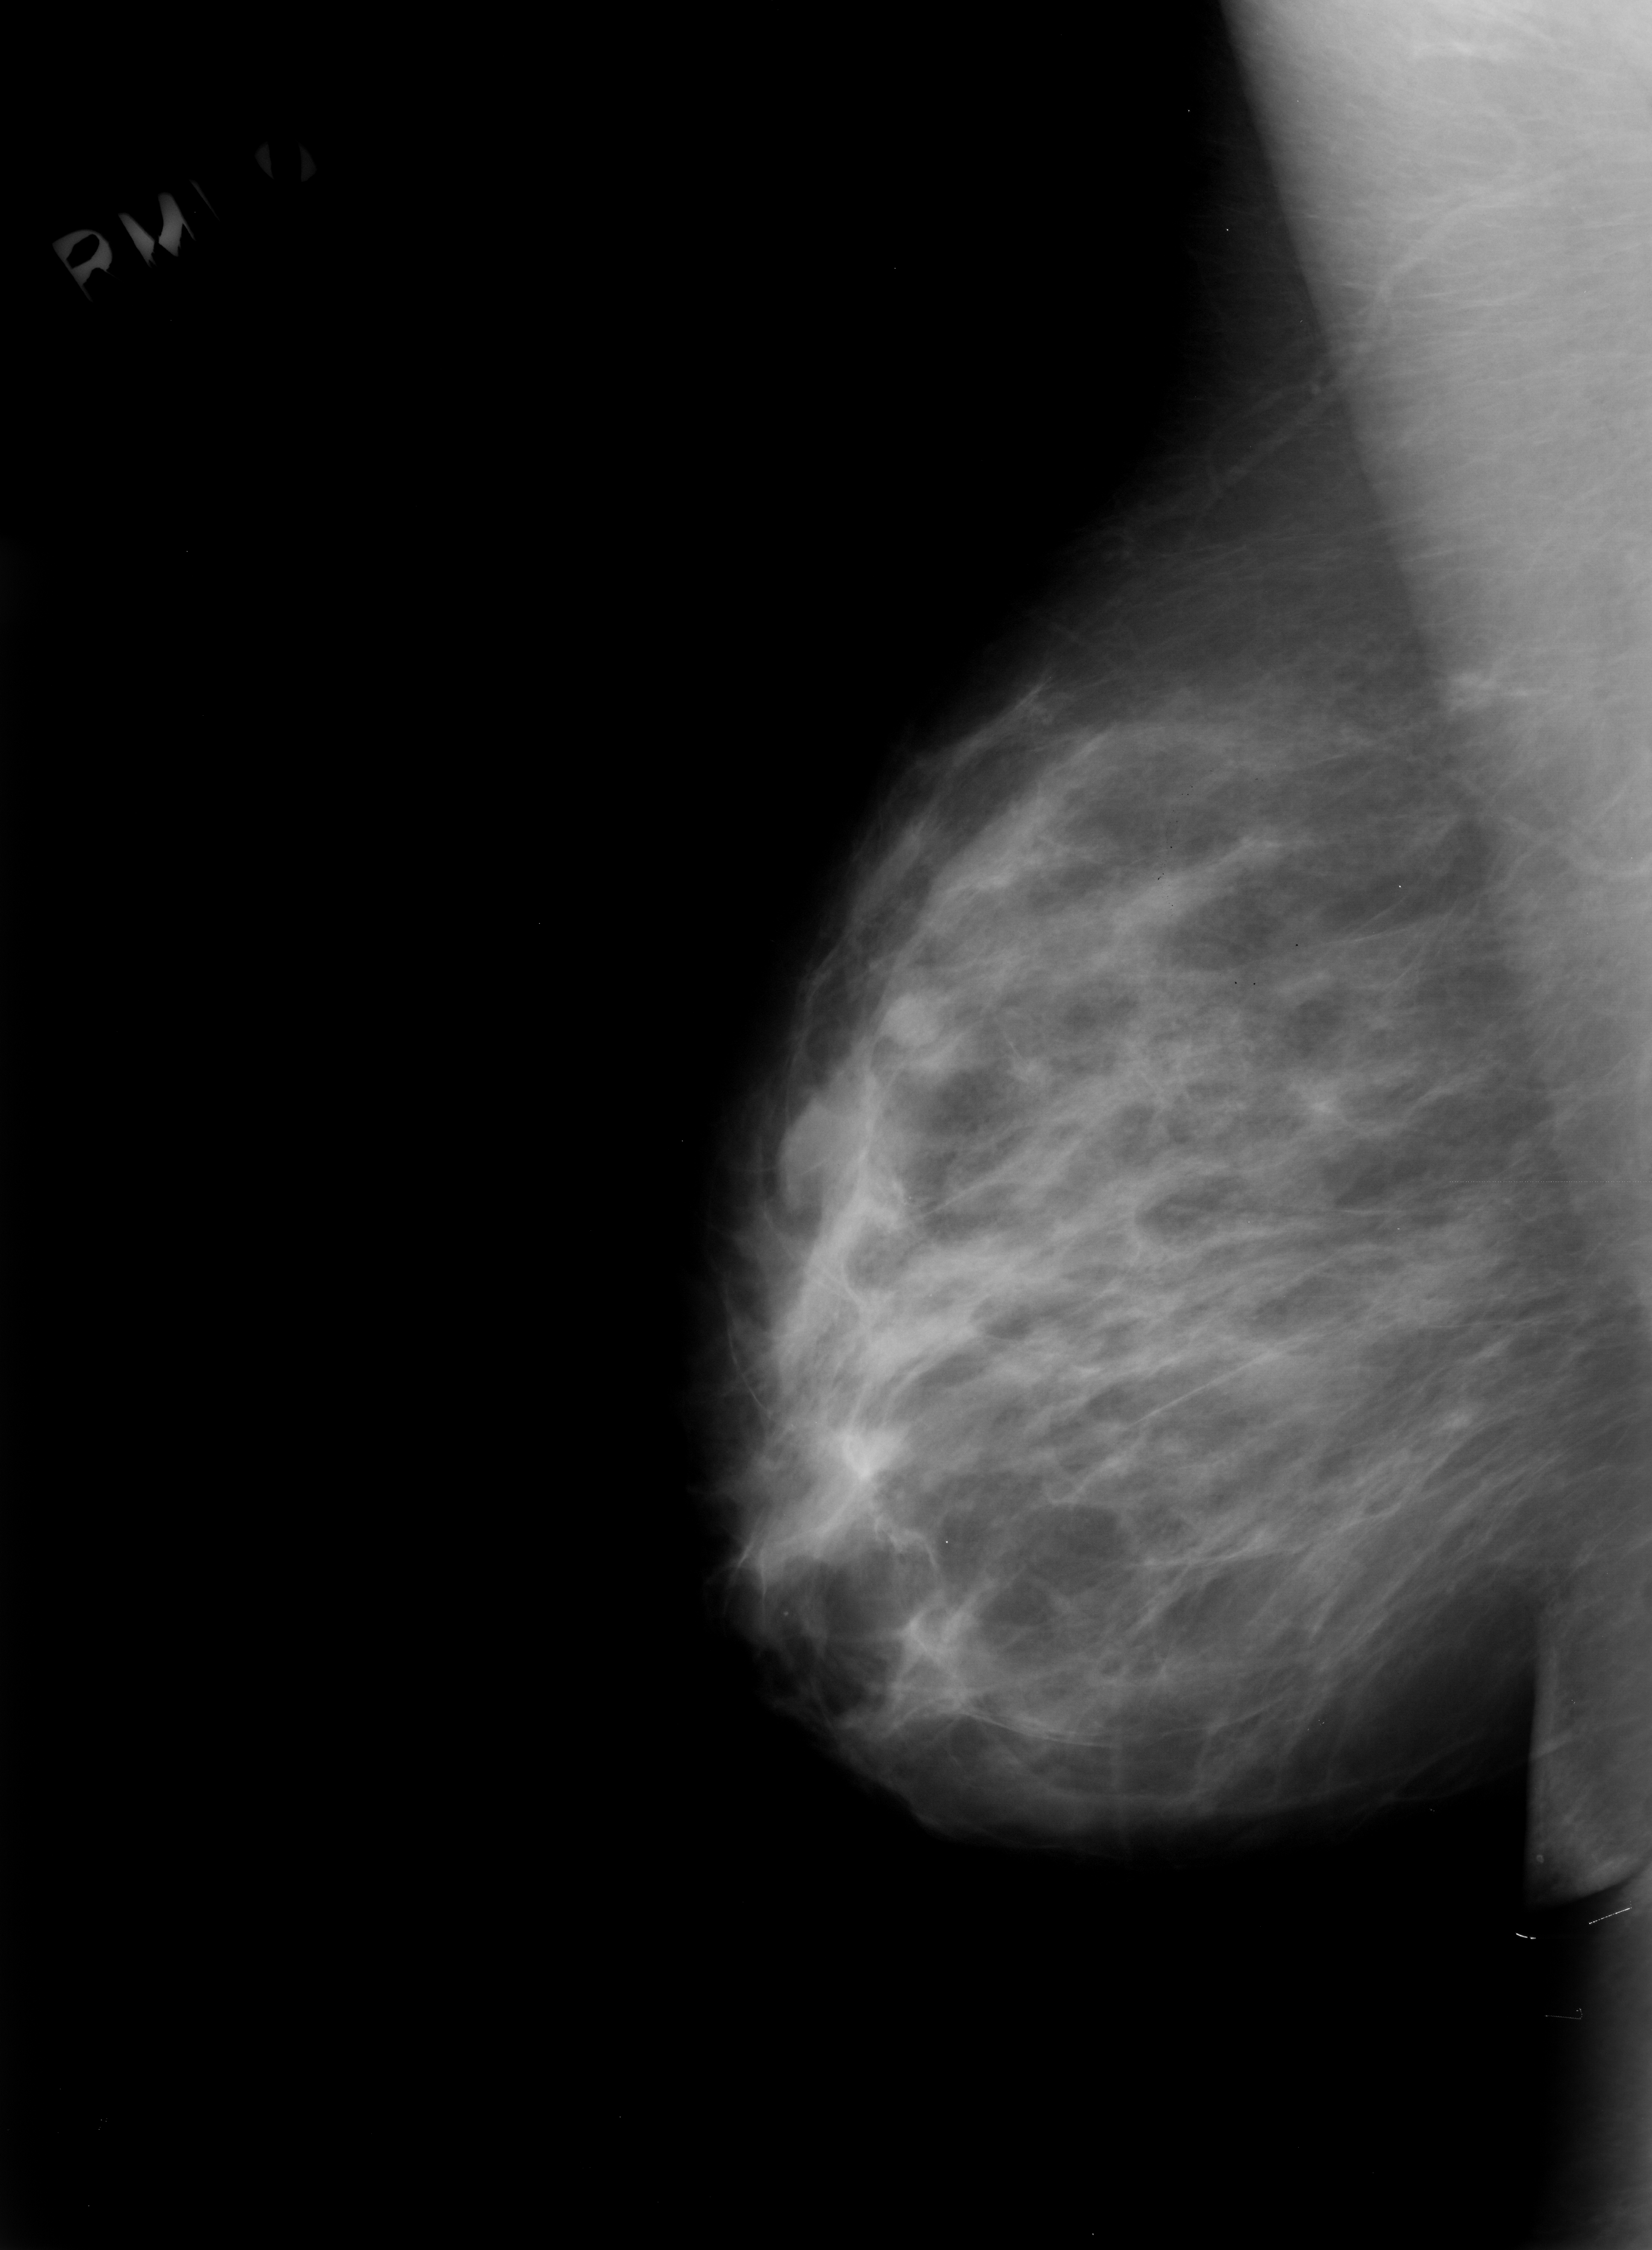
Scanned film-screen mammogram, right breast, mediolateral oblique (MLO) view, BI-RADS breast density category 2 (scale 1–4).
Abnormality record for this image: mass, shape oval, margins circumscribed; BI-RADS assessment category 3; subtlety rating 4 on a 1 (subtle) to 5 (obvious) scale; pathology (as recorded): benign.